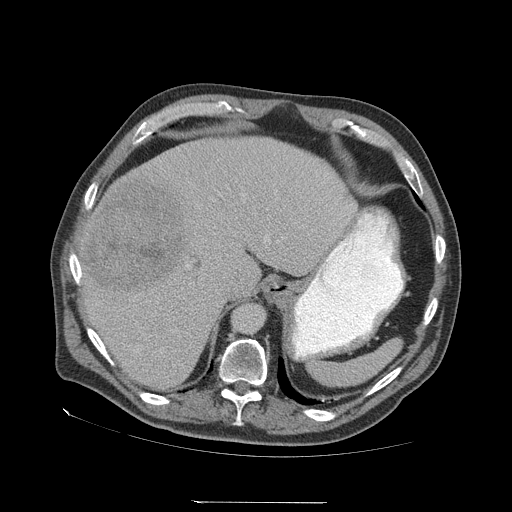
Contrast-enhanced abdominal CT (liver protocol), one axial slice. Slice 49 of 83 in the series (ordered by position). 140 kVp. Soft-tissue window (W 400 / L 40 HU). 2.5 mm slice thickness. 512 × 512 image matrix. Case-level facts recorded for this patient, not image findings: diagnosis: hepatocellular carcinoma (patient treated with transarterial chemoembolisation; whether this scan precedes or follows treatment is not stated here); TNM stage (as recorded): Stage-I; Child-Pugh class: A.
Annotated regions visible in this slice (semi-automatically segmented with operator editing):
- liver parenchyma outside the tumour (the mass and vessels are separate outlines, so this box may not span the whole liver): bounding box (x1, y1, x2, y2) in pixels: (78, 136, 356, 389)
- mass: (84, 178, 189, 300)
- liver vessels: (186, 195, 244, 267)